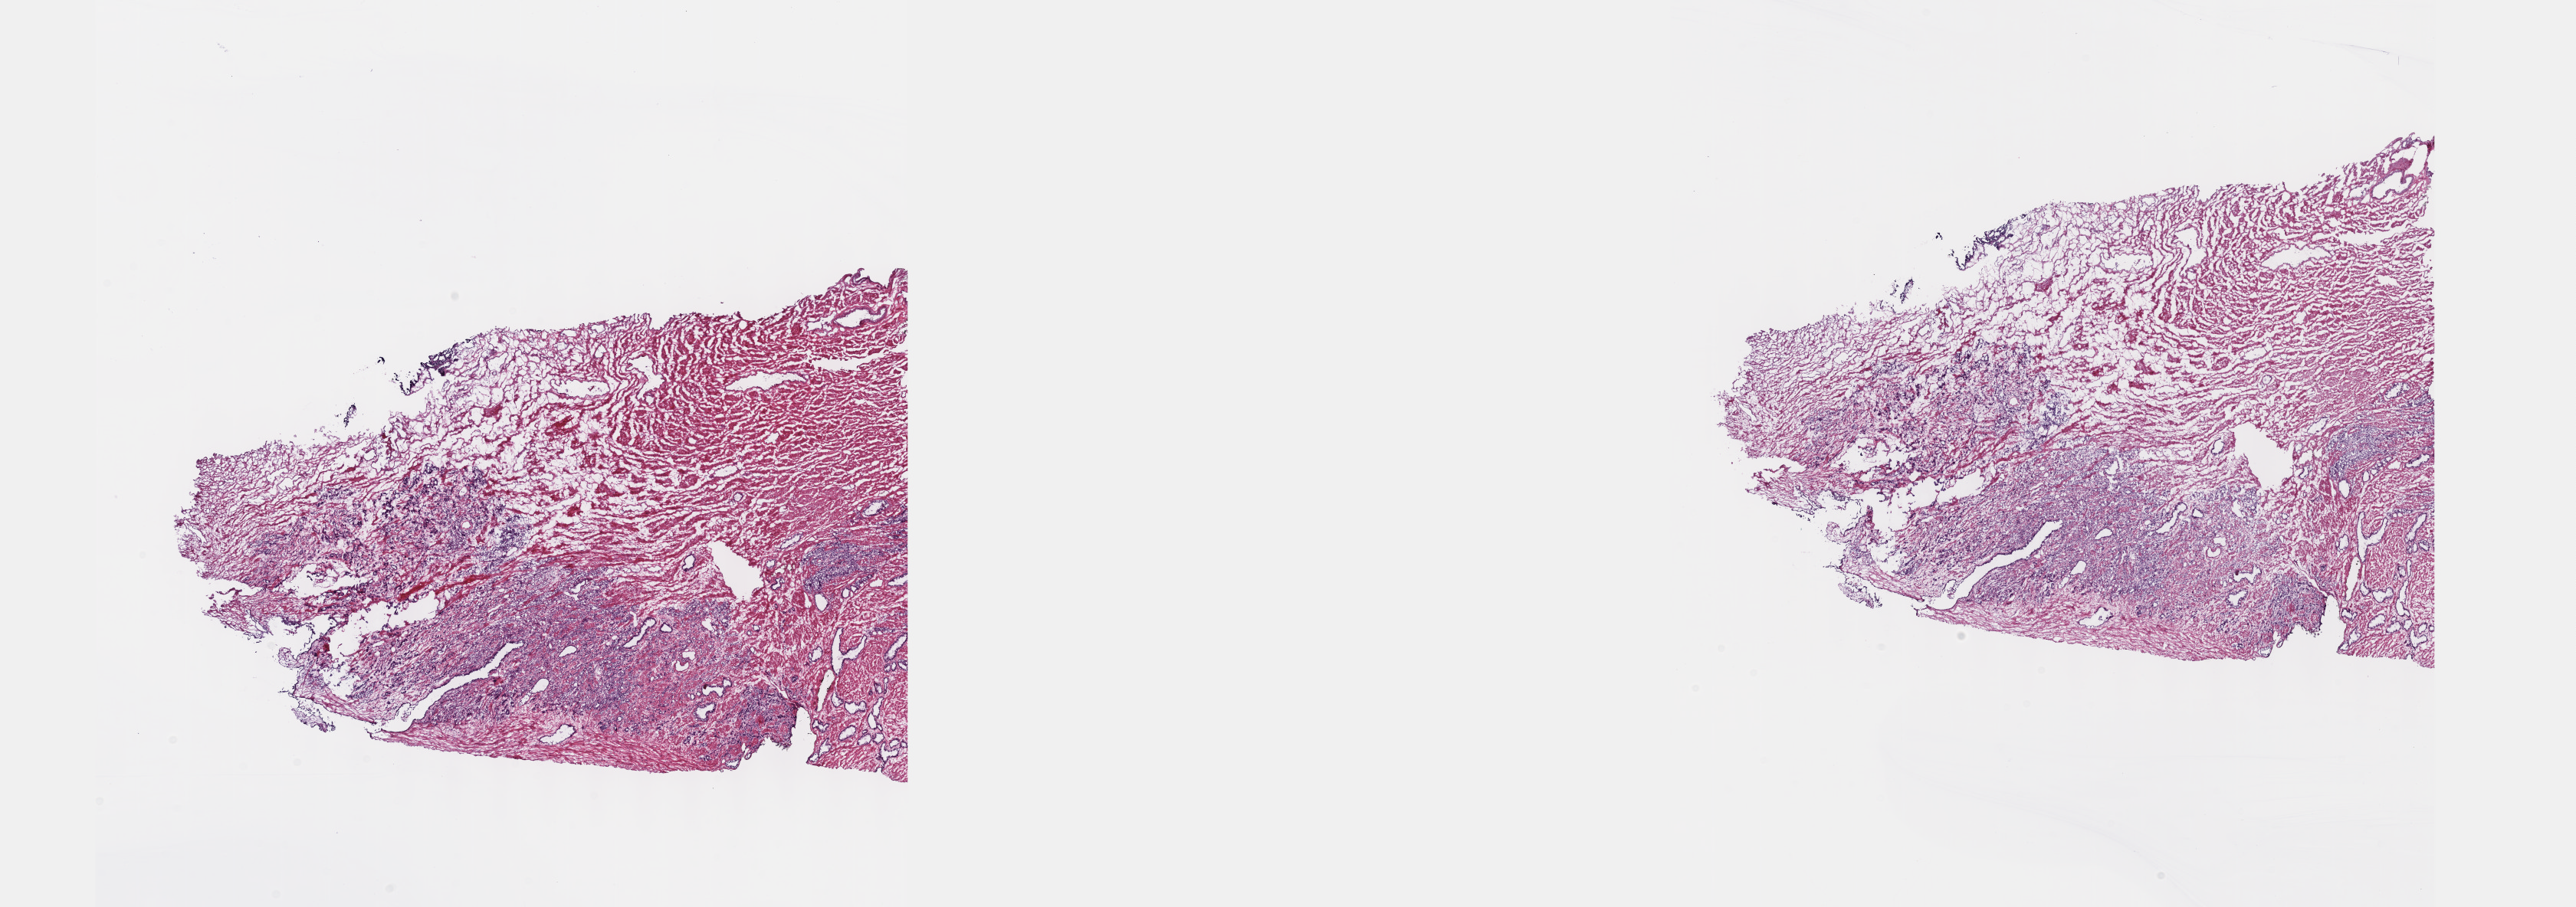
Digitized H&E tissue section (whole slide), a low-resolution overview of the entire scanned area, about 27.2 x 9.6 mm (acquisition: 40x scan); frozen section; sample: primary tumour, prostate. Male, age 67 years at initial diagnosis. Gleason score: 9 (4+5). Pathologist review of this section (percent, as recorded): tumour cells 50%, tumour nuclei 60%, normal cells 40%, stromal cells 10%, necrosis 0%. Inflammatory infiltration, as recorded: lymphocyte infiltration 0%, monocyte infiltration 0%, neutrophil infiltration 0%.
* lymph nodes positive (case pathology): 4 of 20 examined
* pathologic diagnosis: Adenocarcinoma, NOS
* laterality: bilateral